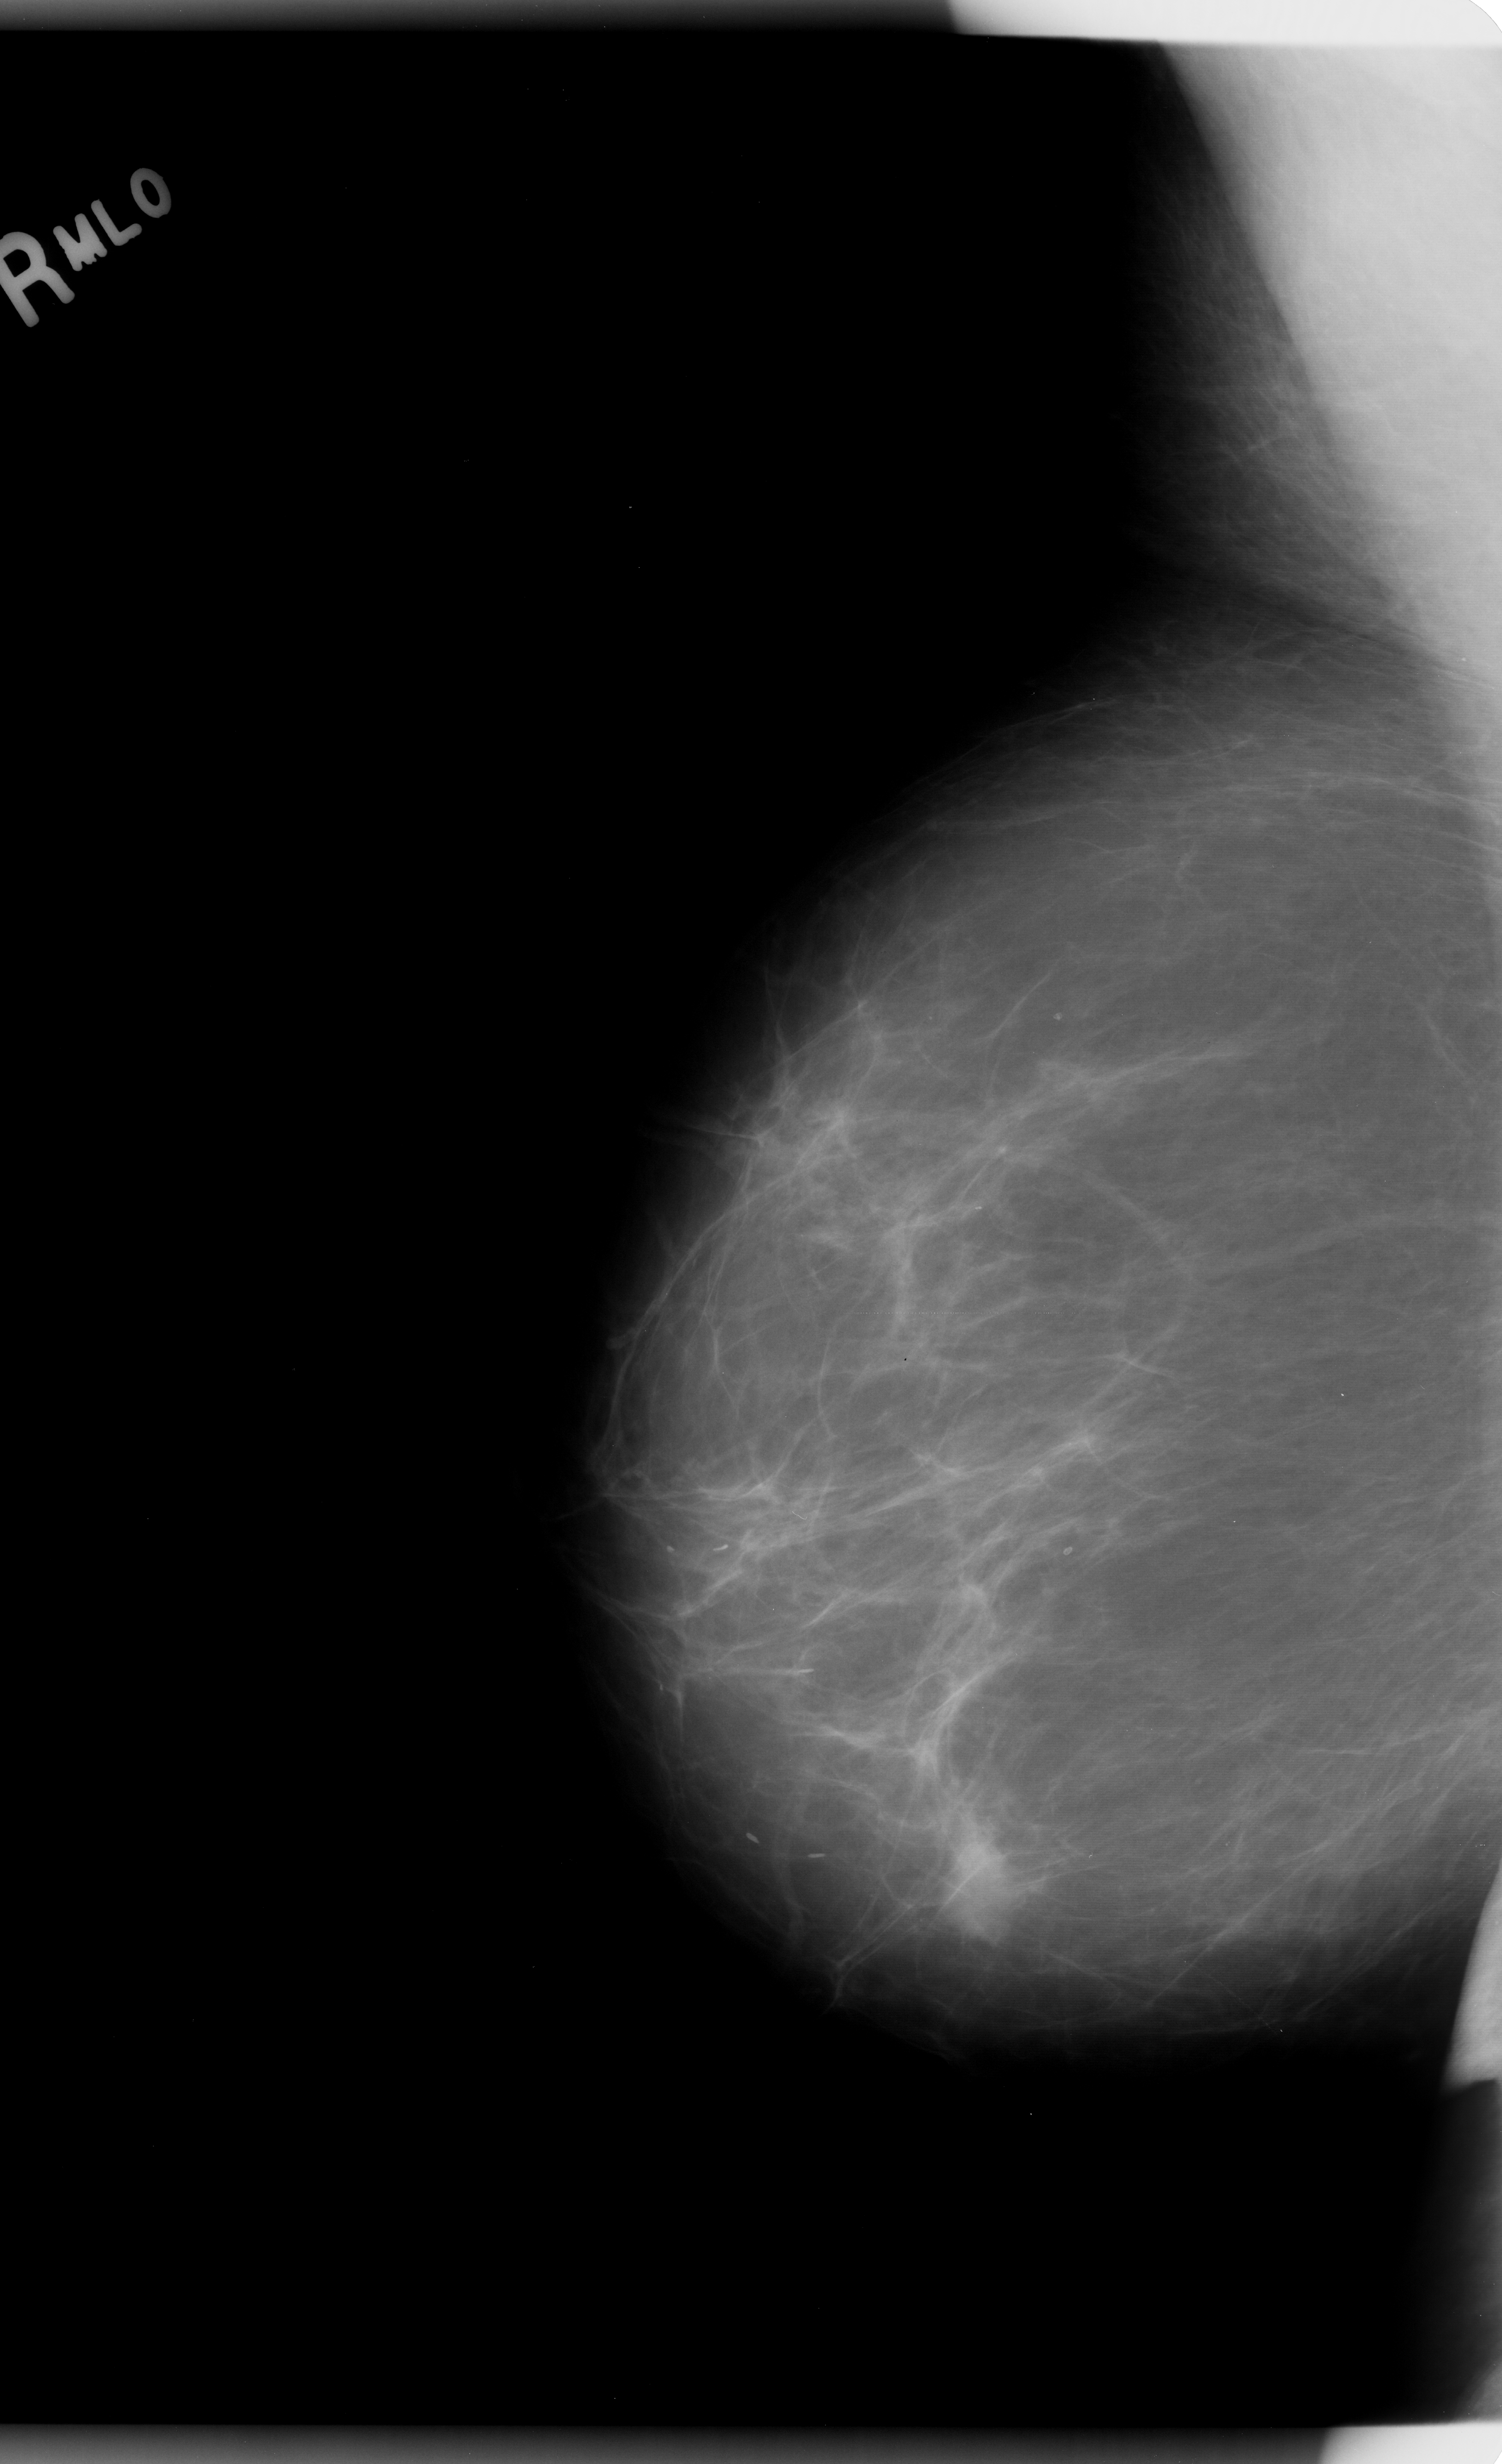
Digitized screen-film mammogram; right breast; mediolateral oblique (MLO) view; breast composition: almost entirely fatty (BI-RADS density category 1 of 4).
Mass, shape oval, margins microlobulated; BI-RADS assessment category 5; pathology (as recorded): malignant.